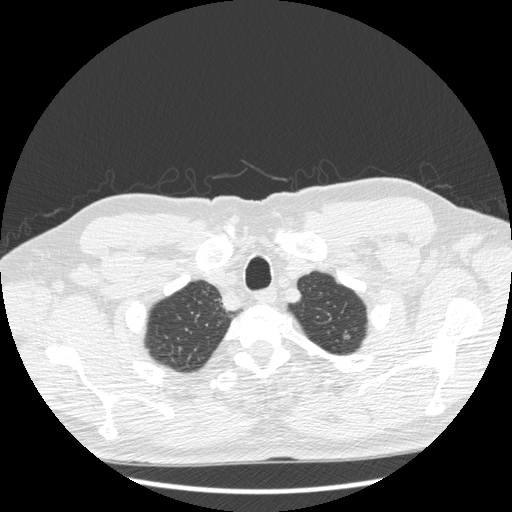
Low-dose screening chest CT, one axial slice; 120 kVp; lung window (W 1500 / L -600 HU); 1.25 mm slice thickness; 512 × 512 image matrix, field of view 380 × 380 mm.
Structures marked on this image (manually delineated by an expert):
- lesion 1 (tumor, upper lobe of left lung): bounding box [x1, y1, x2, y2] px = [343, 334, 350, 339]